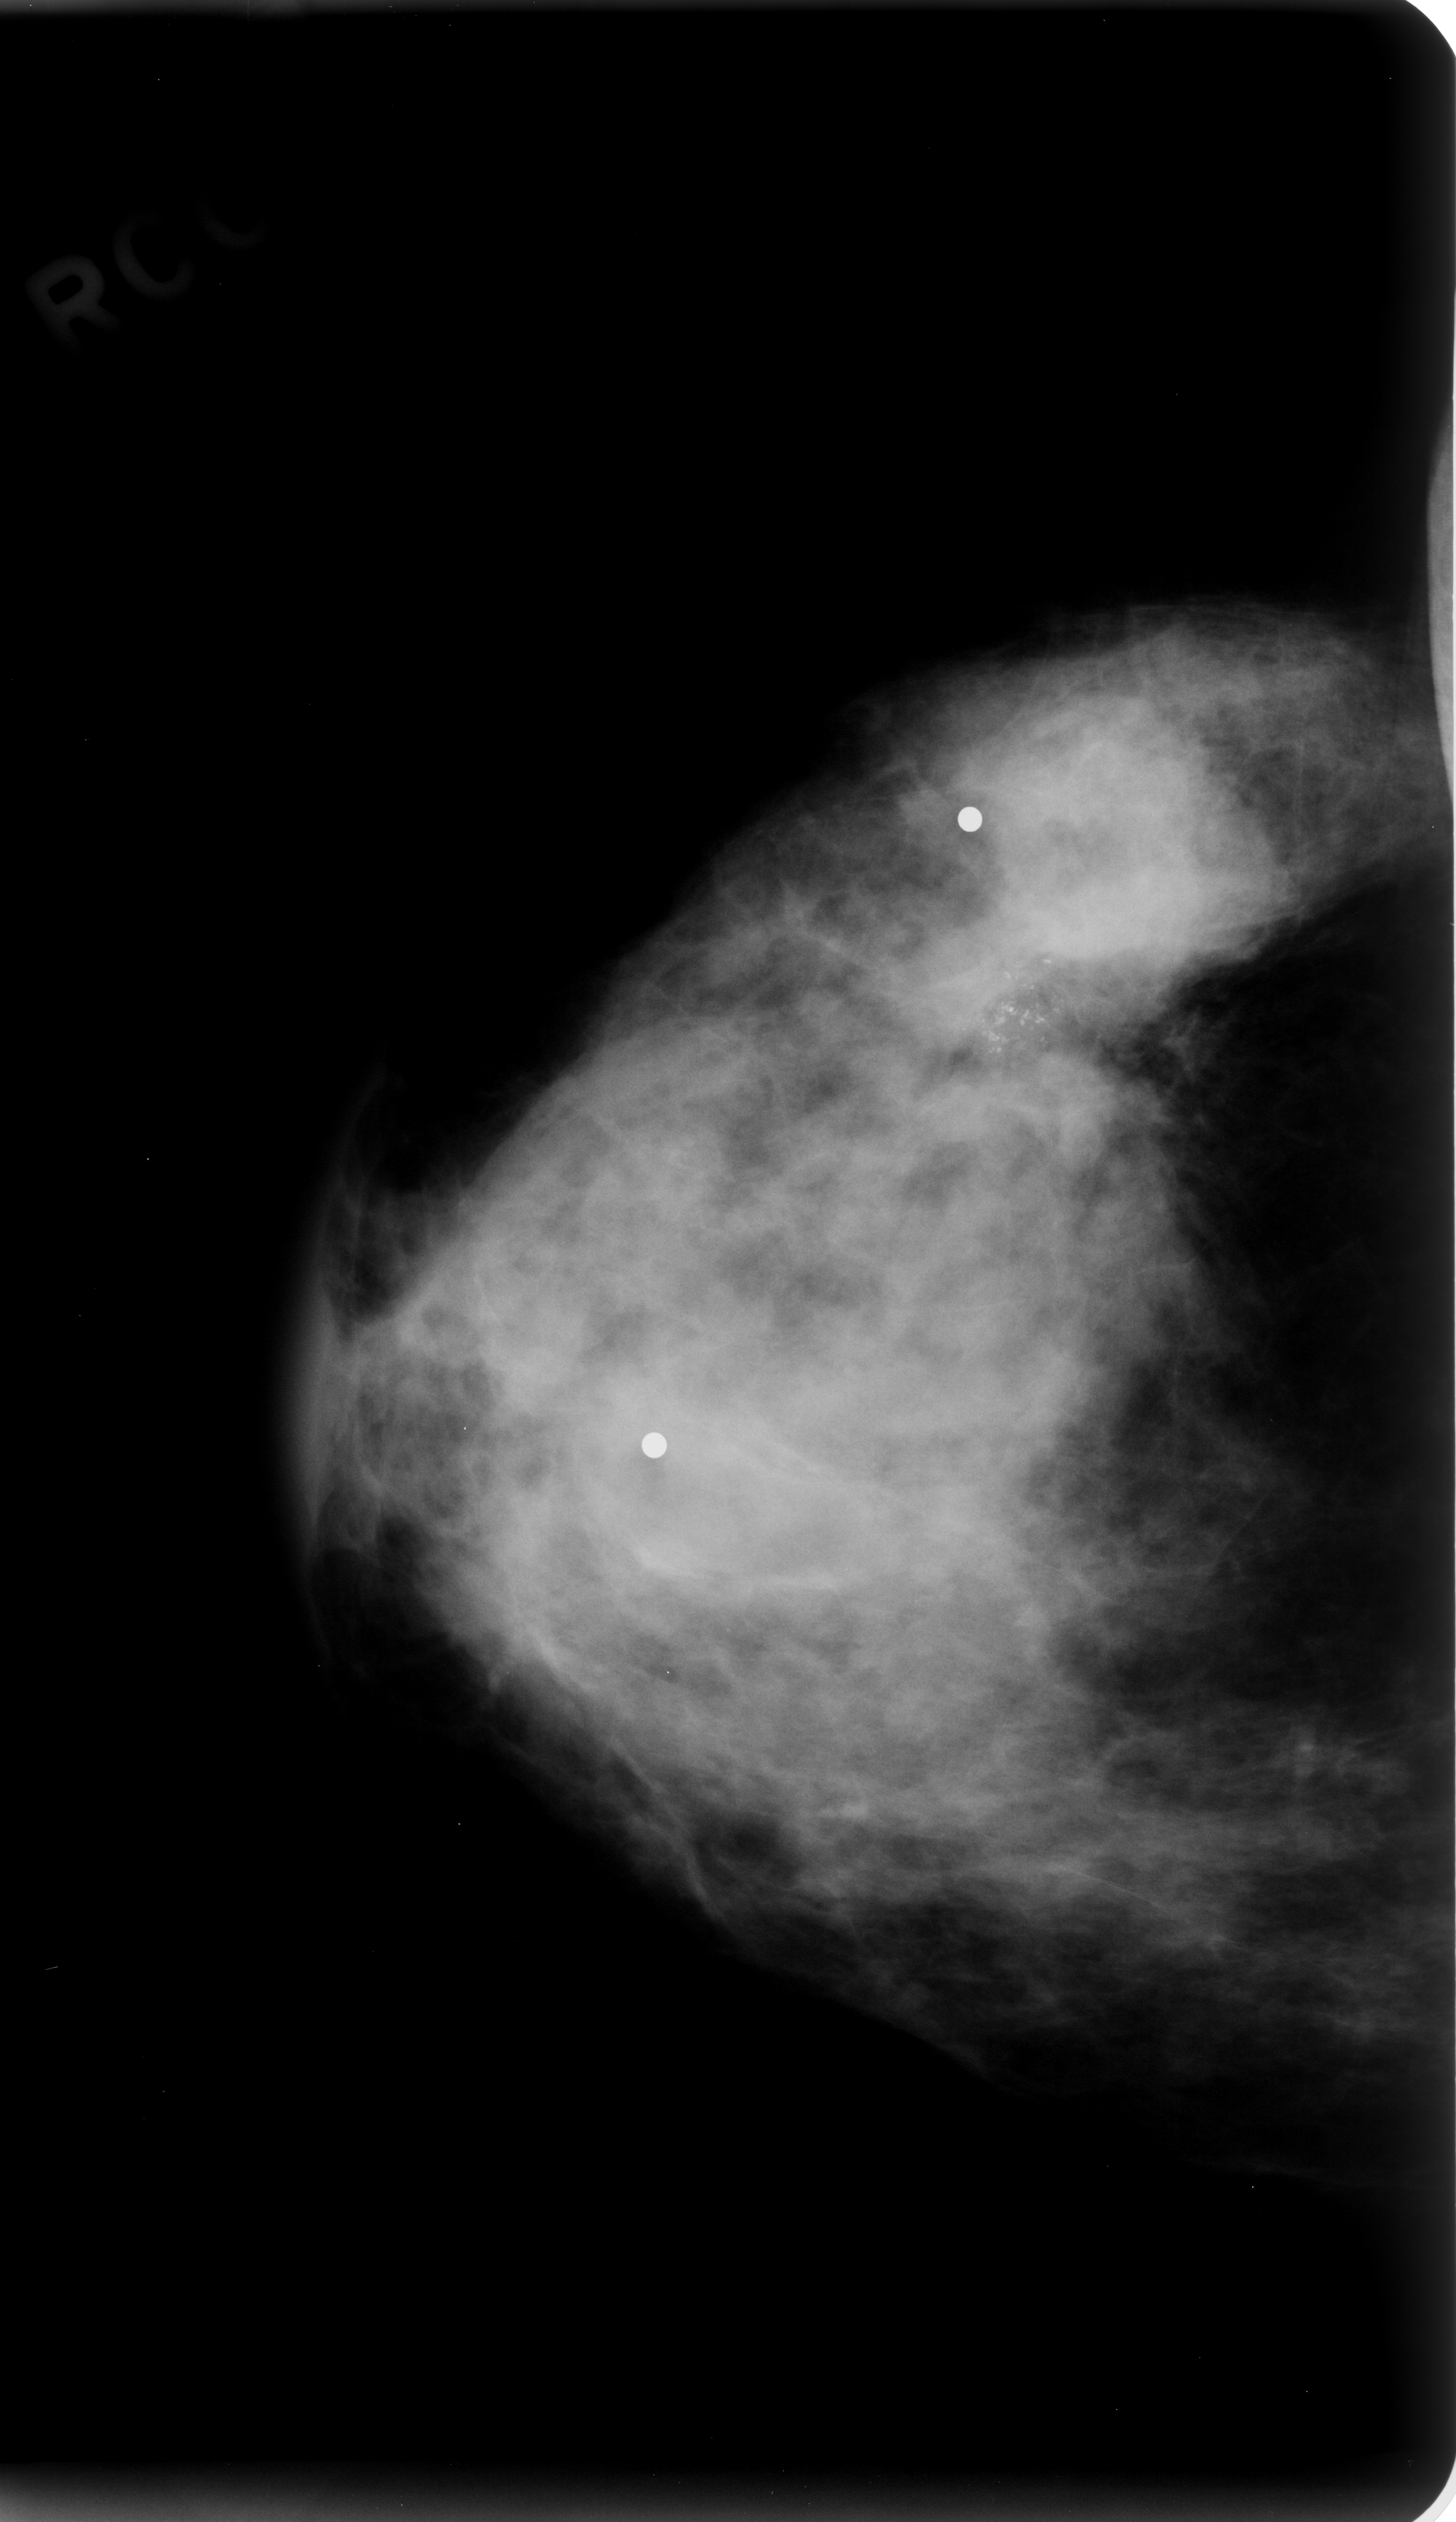
Mammogram (digitized film); right breast; craniocaudal (CC) view; BI-RADS breast density category 3 (scale 1–4).
- Finding: calcifications, morphology pleomorphic, distribution clustered; BI-RADS assessment category 5; pathology (as recorded): malignant.